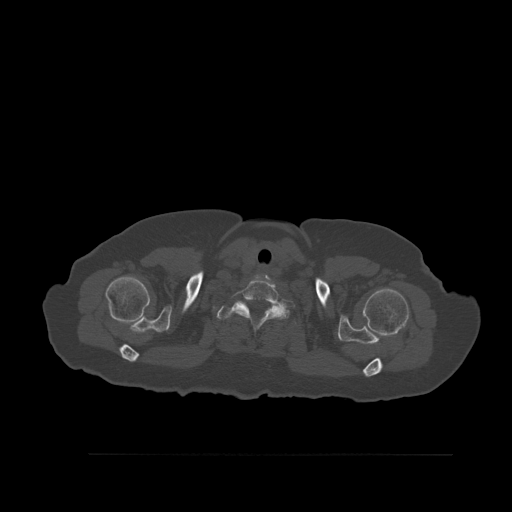
CT including the spine, one axial slice. Position 450 of 527 along the scan axis. Bone window (W 1800 / L 400 HU). 512 × 512 image matrix. Female patient, age 73 years. Case-level facts recorded for this patient, not image findings: primary cancer: breast.
Annotated regions visible in this slice (semi-automatically segmented with operator editing):
- T1 vertebra: bounding box (x1, y1, x2, y2) in pixels: (217, 304, 297, 326)